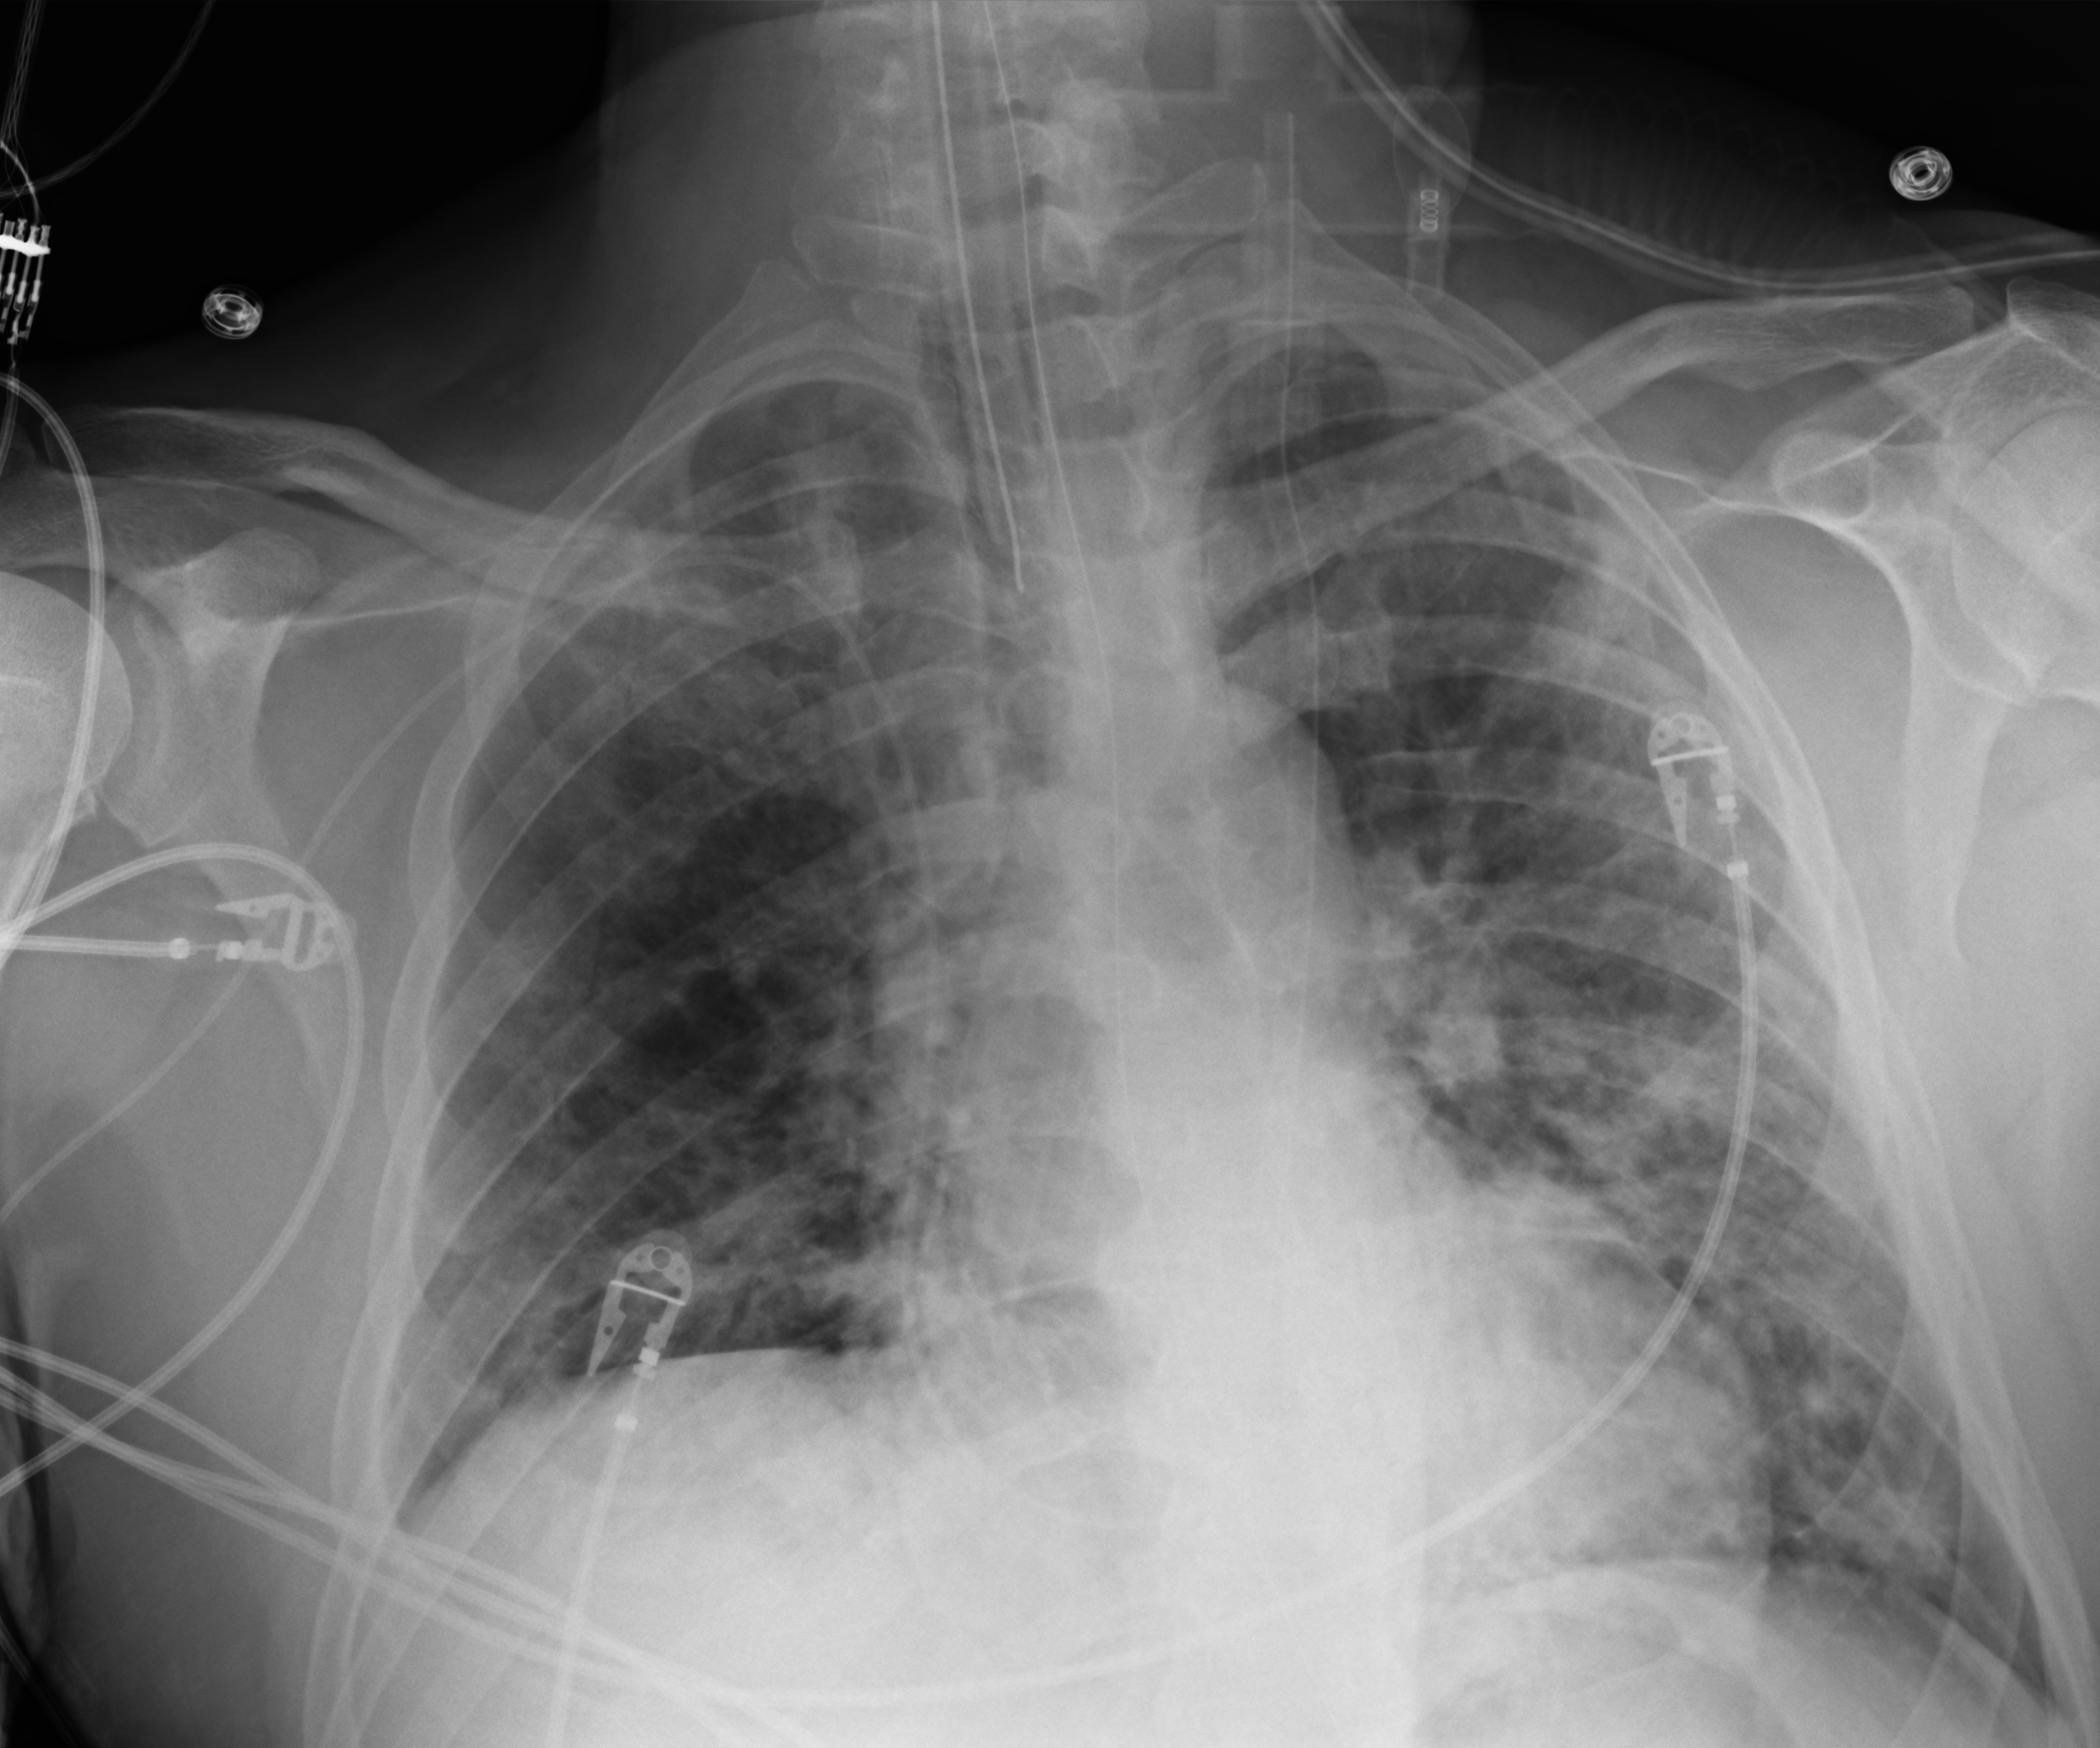
Chest X-ray (portable); anteroposterior (AP) projection. Male patient hospitalised with COVID-19, age 18–59 years.
From the hospital-stay record, not from the radiograph (when in the stay this image was taken is not recorded):
- admitted to intensive care during this hospital stay: no